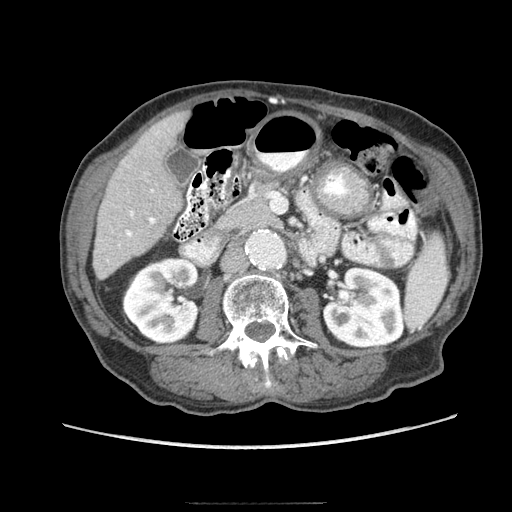
Contrast-enhanced abdominal CT (liver protocol), one axial slice. Position 28 of 83 along the scan axis. Reconstruction kernel STANDARD. Soft-tissue window (W 400 / L 40 HU). 2.5 mm slice thickness. 512 × 512 image matrix. From the clinical record (not read from this slice): diagnosis: hepatocellular carcinoma (patient treated with transarterial chemoembolisation; whether this scan precedes or follows treatment is not stated here); TNM stage (as recorded): Stage-I; Child-Pugh class: A; tumour differentiation: moderately differentiated.
Annotated regions visible in this slice (semi-automatic segmentation, software-assisted and operator-edited):
- liver parenchyma outside the tumour (the mass and vessels are separate outlines, so this box may not span the whole liver): bounding box (x1, y1, x2, y2) in pixels: (92, 110, 188, 279)
- liver vessels: (126, 189, 155, 237)